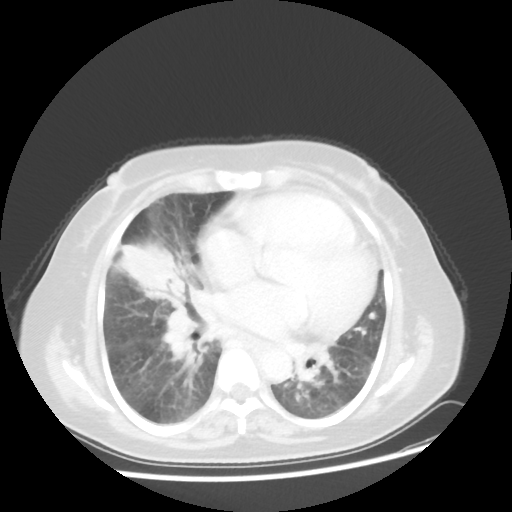
Chest CT, one axial slice. Position 21 of 45 along the scan axis. Lung window (W 1500 / L -600 HU). 512 × 512 image matrix, field of view 359 × 359 mm. Female patient, age 67 years. From the clinical record (not read from this slice): clinical TNM (as recorded): T2a N3 M1a.
Outlined on this slice (bounding box drawn by a radiologist):
- lung tumour (recorded histology: adenocarcinoma): bounding box (x1, y1, x2, y2) in pixels: (121, 245, 186, 299)